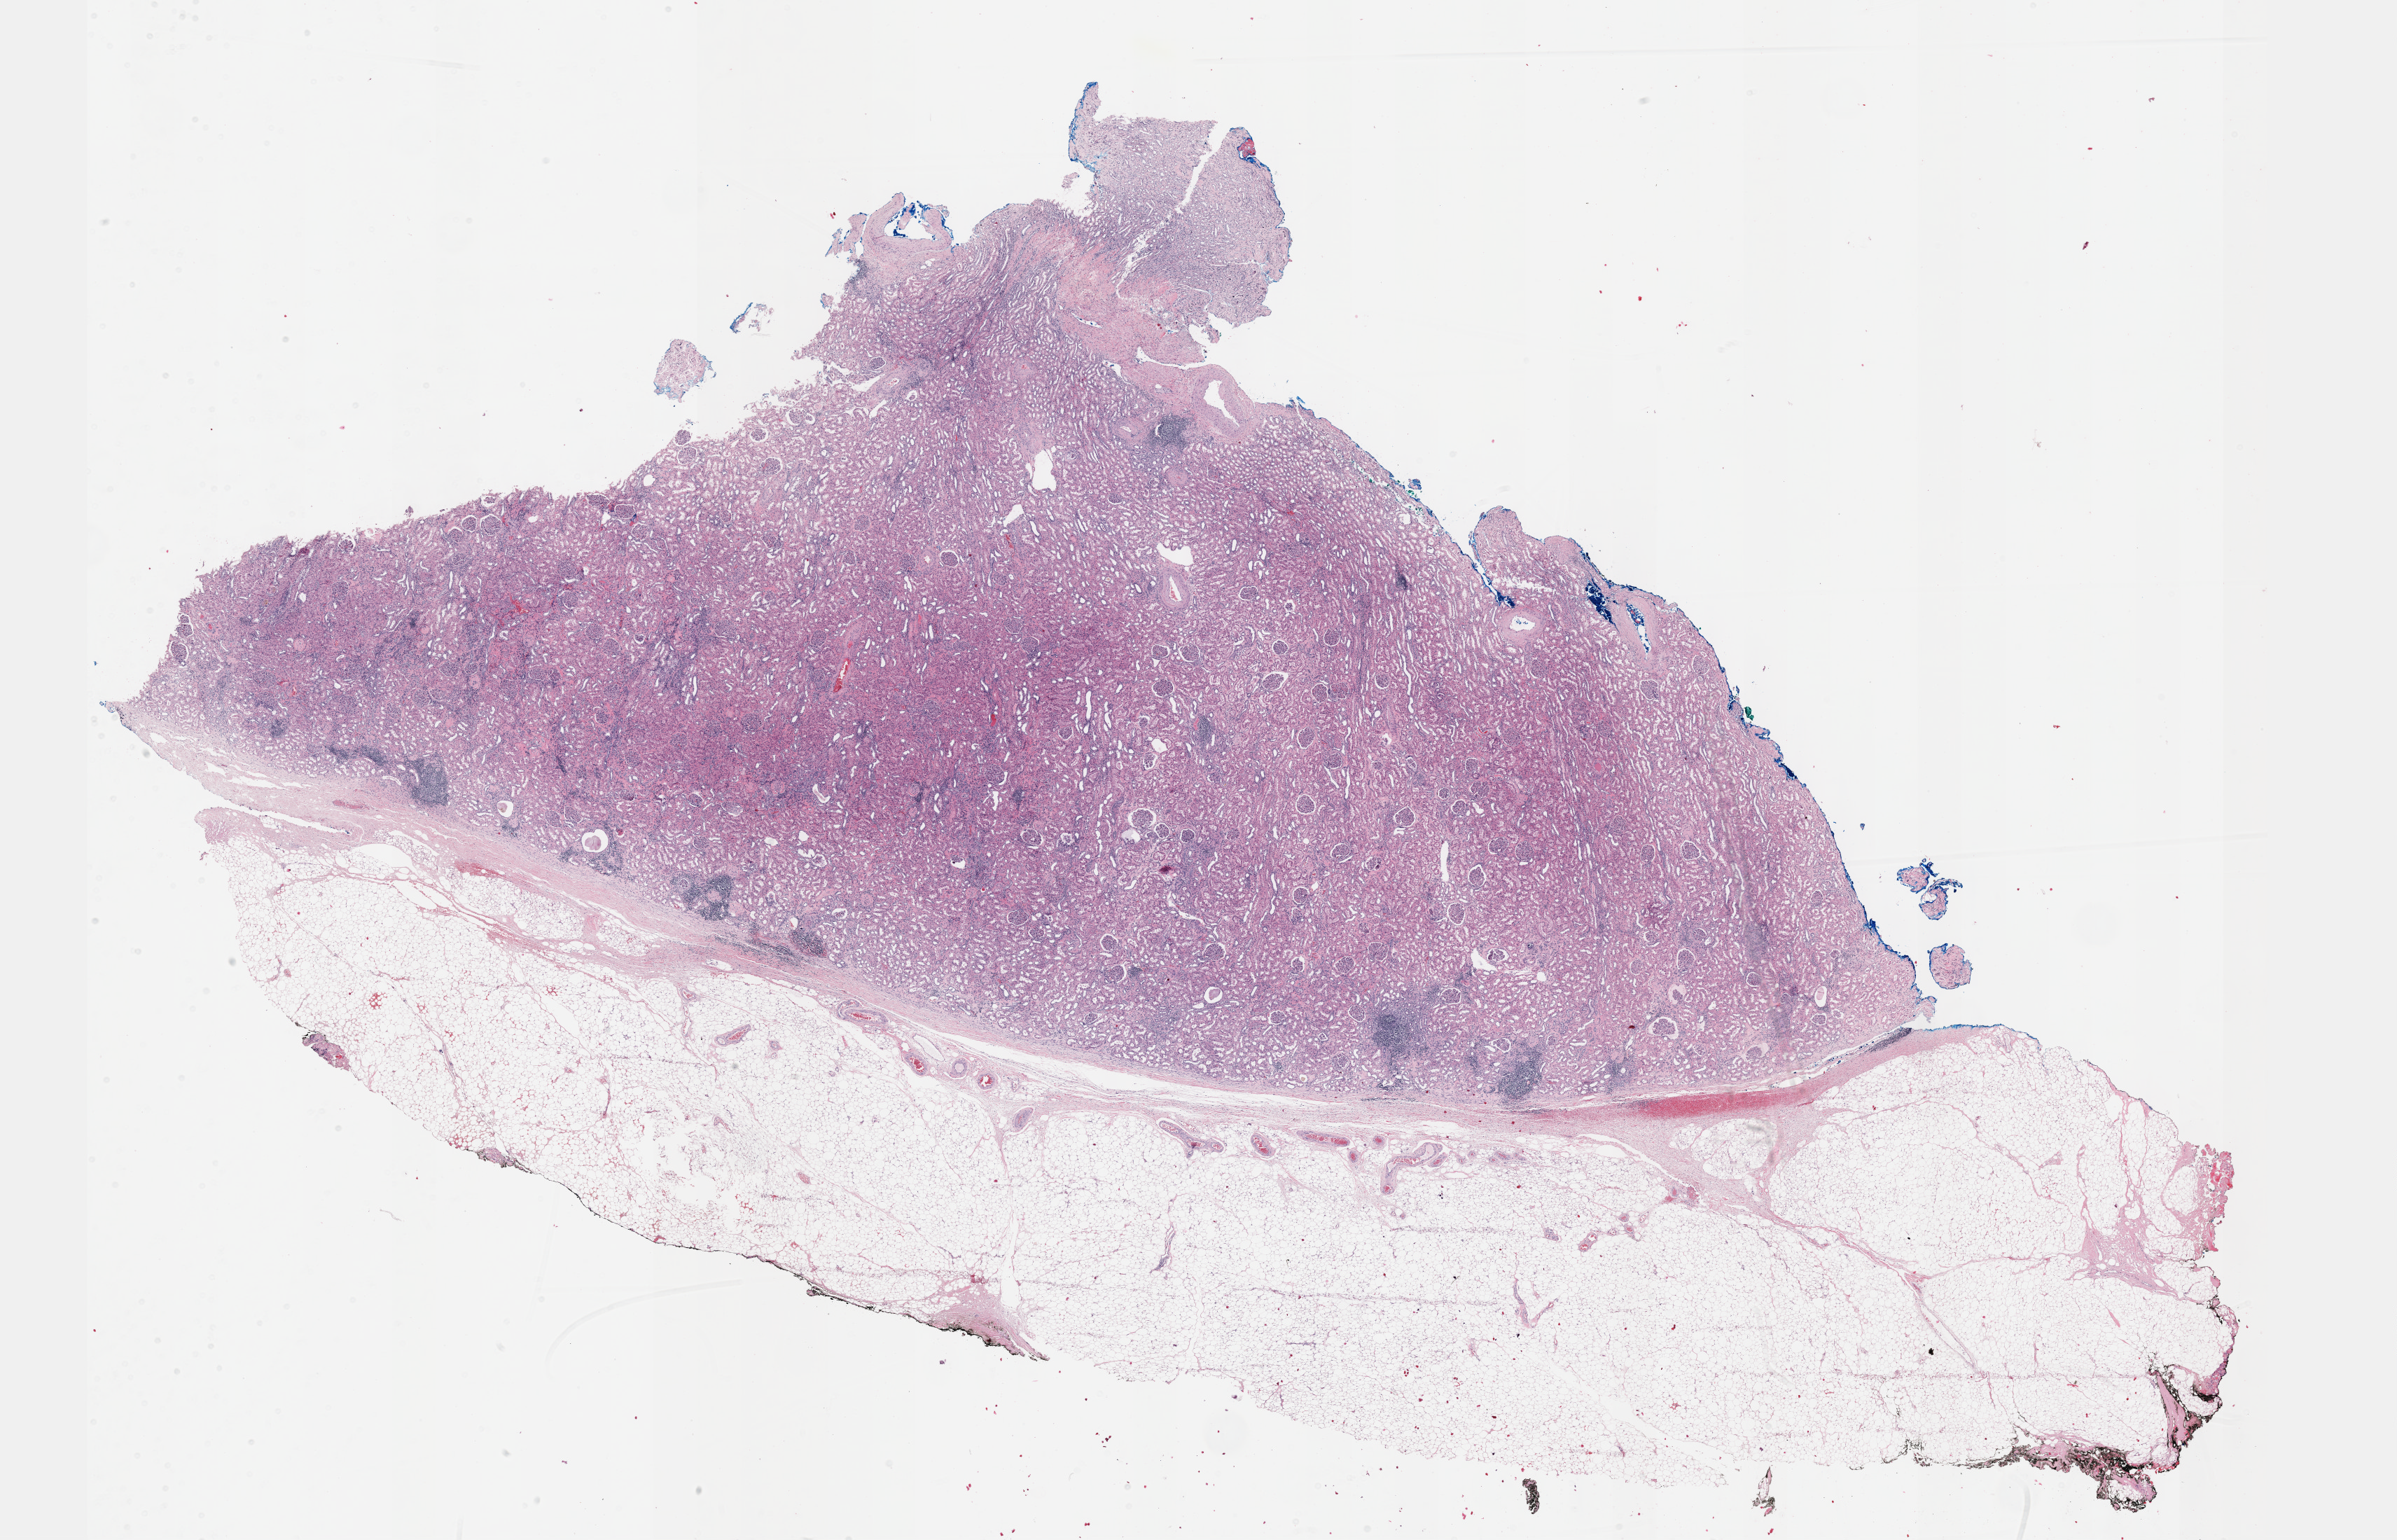
Digitized H&E-stained tissue section (whole slide), whole scanned area (about 27.7 x 17.8 mm) shown as a low-resolution overview, formalin-fixed paraffin-embedded (FFPE) diagnostic section, primary tumour sample from the kidney. Male patient; age at initial diagnosis 65 years.
* pathologic diagnosis: Papillary adenocarcinoma, NOS
* laterality: right
* AJCC pathologic stage: I (7th edition)